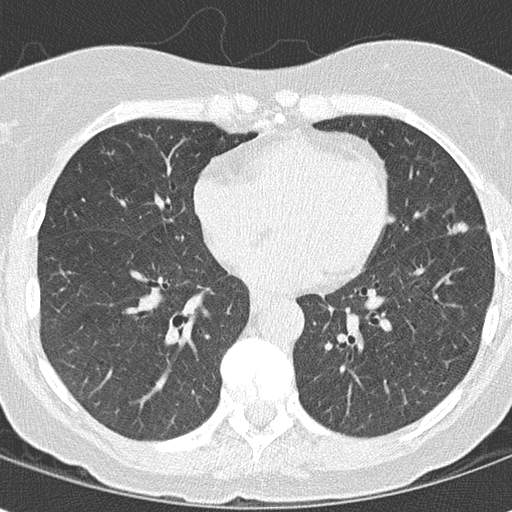
Axial slice from a low-dose chest CT screening exam, second screening round (one year after baseline), lung window (W 1500 / L -600 HU), 2 mm slice thickness, lung (sharp) reconstruction kernel (B50f). Female, age 63 years at enrolment. Current smoker at enrolment.
- Lesion marked by an expert reader, bounding box <428,202,482,255> (left, top, right, bottom; pixels).
- The screening reader recorded 4 non-calcified nodules or masses ≥4 mm on this exam (right upper lobe, left lower lobe, left upper lobe, lingula); which of them this box marks is not recorded.
- Participant outcome: lung cancer diagnosed 504 days after this screen (after the third annual screen) — bronchiolo-alveolar adenocarcinoma, NOS, lingula, stage IA (AJCC 6th edition), 14 mm at pathology.